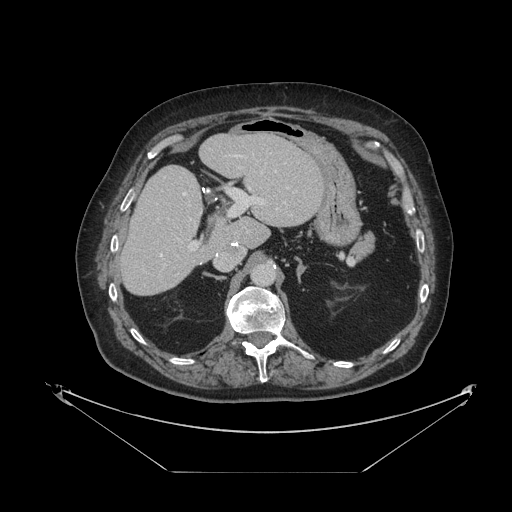
Contrast-enhanced abdominal CT, one axial slice. Reconstruction kernel STANDARD. Intravenous contrast given. Soft-tissue window (W 400 / L 40 HU). 2.5 mm slice thickness. 512 × 512 image matrix, field of view 500 × 500 mm. Male patient, age 68 years. Case-level facts recorded for this patient, not image findings: diagnosis: colorectal cancer liver metastases, imaged before liver resection; multiple liver metastases: no; largest metastasis: 4 cm.
Structures marked on this image (expert manual segmentation):
- hepatic veins: bounding box (x1, y1, x2, y2) in pixels: (160, 155, 288, 257)
- liver: (122, 135, 323, 295)
- planned liver remnant (the part of the liver to remain after resection): (122, 135, 323, 295)
- portal vein (with intrahepatic branches): (189, 189, 285, 251)